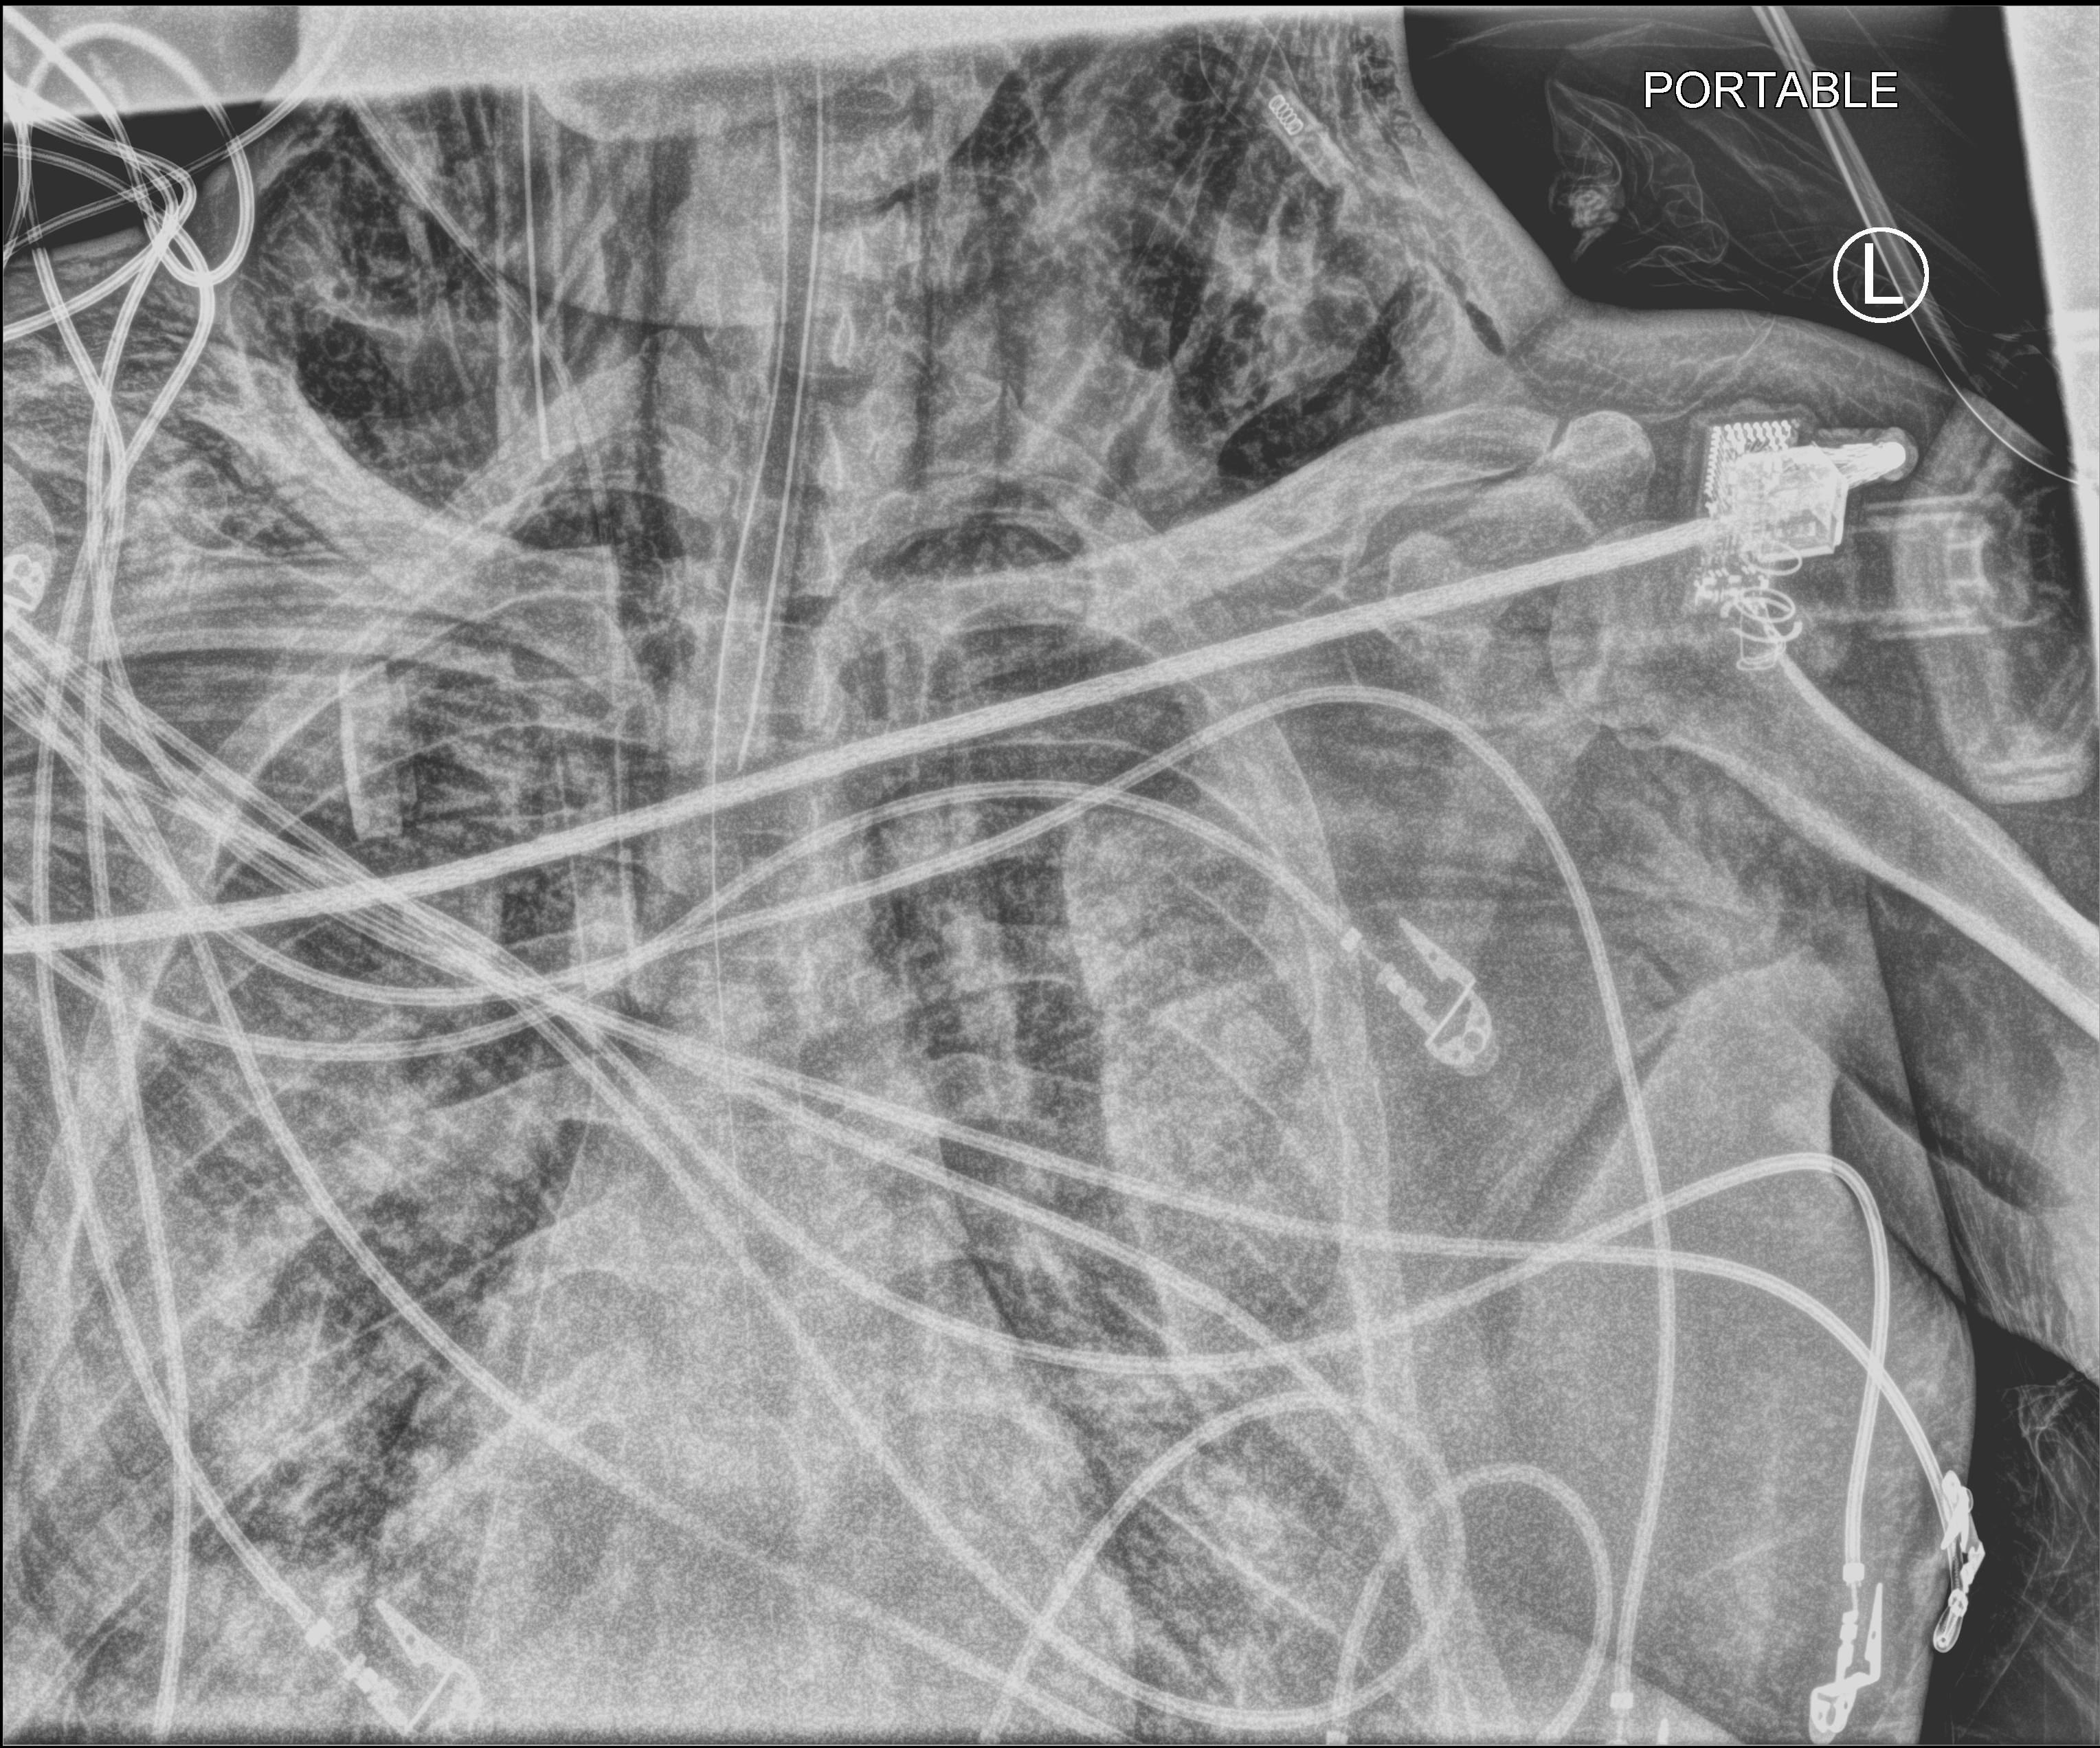
Bedside chest radiograph (computed radiography), anteroposterior (AP) projection. Patient hospitalised with COVID-19, aged 18–59 years.
Hospital-stay facts (about this admission, not read from this image; timing relative to this image not recorded):
- COPD (admission record): no